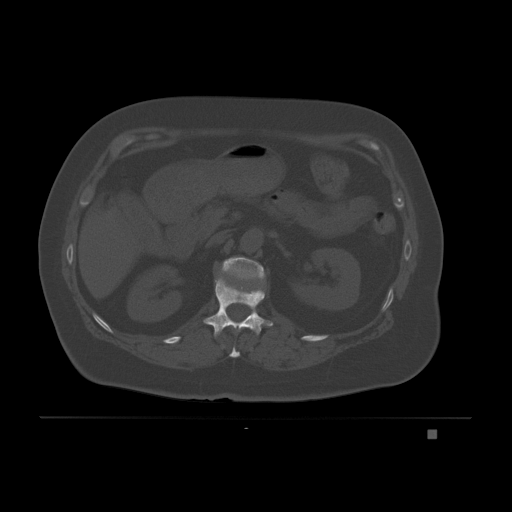
CT including the spine, one axial slice; slice 79 of 221 in the series (ordered by position); bone window (W 1800 / L 400 HU); 512 × 512 image matrix, field of view 474 × 474 mm. Female patient, age 63 years. Case-level facts recorded for this patient, not image findings: primary cancer: breast.
Outlined on this slice (semi-automatic segmentation, software-assisted and operator-edited):
- L1 vertebra: bounding box [x1, y1, x2, y2] px = [220, 257, 265, 292]
- T11 vertebra: [229, 347, 240, 358]
- T12 vertebra: [203, 277, 273, 337]